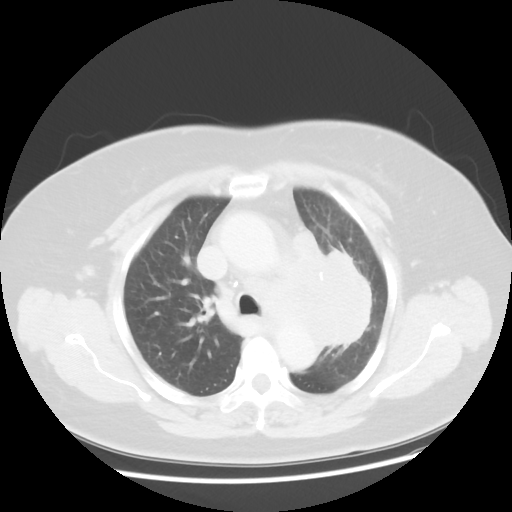
Chest CT, one axial slice. Reconstruction kernel STANDARD. Lung window (W 1500 / L -600 HU). 5 mm slice thickness. 512 × 512 image matrix, field of view 374 × 374 mm. Female patient, age 58 years. From the clinical record (not read from this slice): clinical TNM (as recorded): T4 N3 M0; histopathological grade: G3.
Outlined on this slice (bounding box drawn by a radiologist):
- lung tumour (recorded histology: small cell carcinoma): box from (x=283, y=222) to (x=371, y=356) px